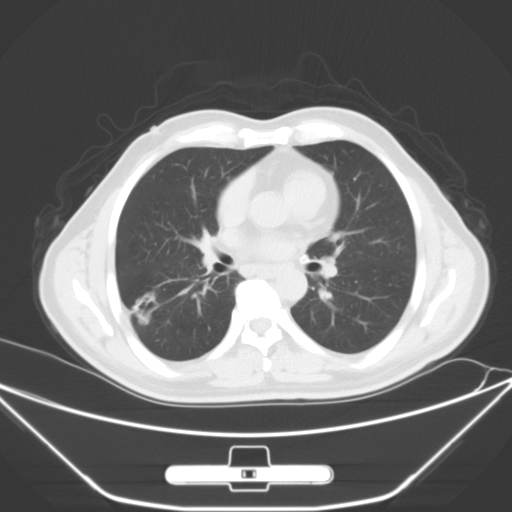
Chest CT, one axial slice; slice 30 of 62 in the series (ordered by position); lung window (W 1500 / L -600 HU); 512 × 512 image matrix. Male patient, age 71 years. Case-level facts recorded for this patient, not image findings: clinical TNM (as recorded): T1c N0 M0; histopathological grade: G2.
Annotated regions visible in this slice (rectangle marked by the reading radiologist):
- lung tumour (recorded histology: adenocarcinoma): bounding box [x1, y1, x2, y2] px = [131, 292, 166, 331]